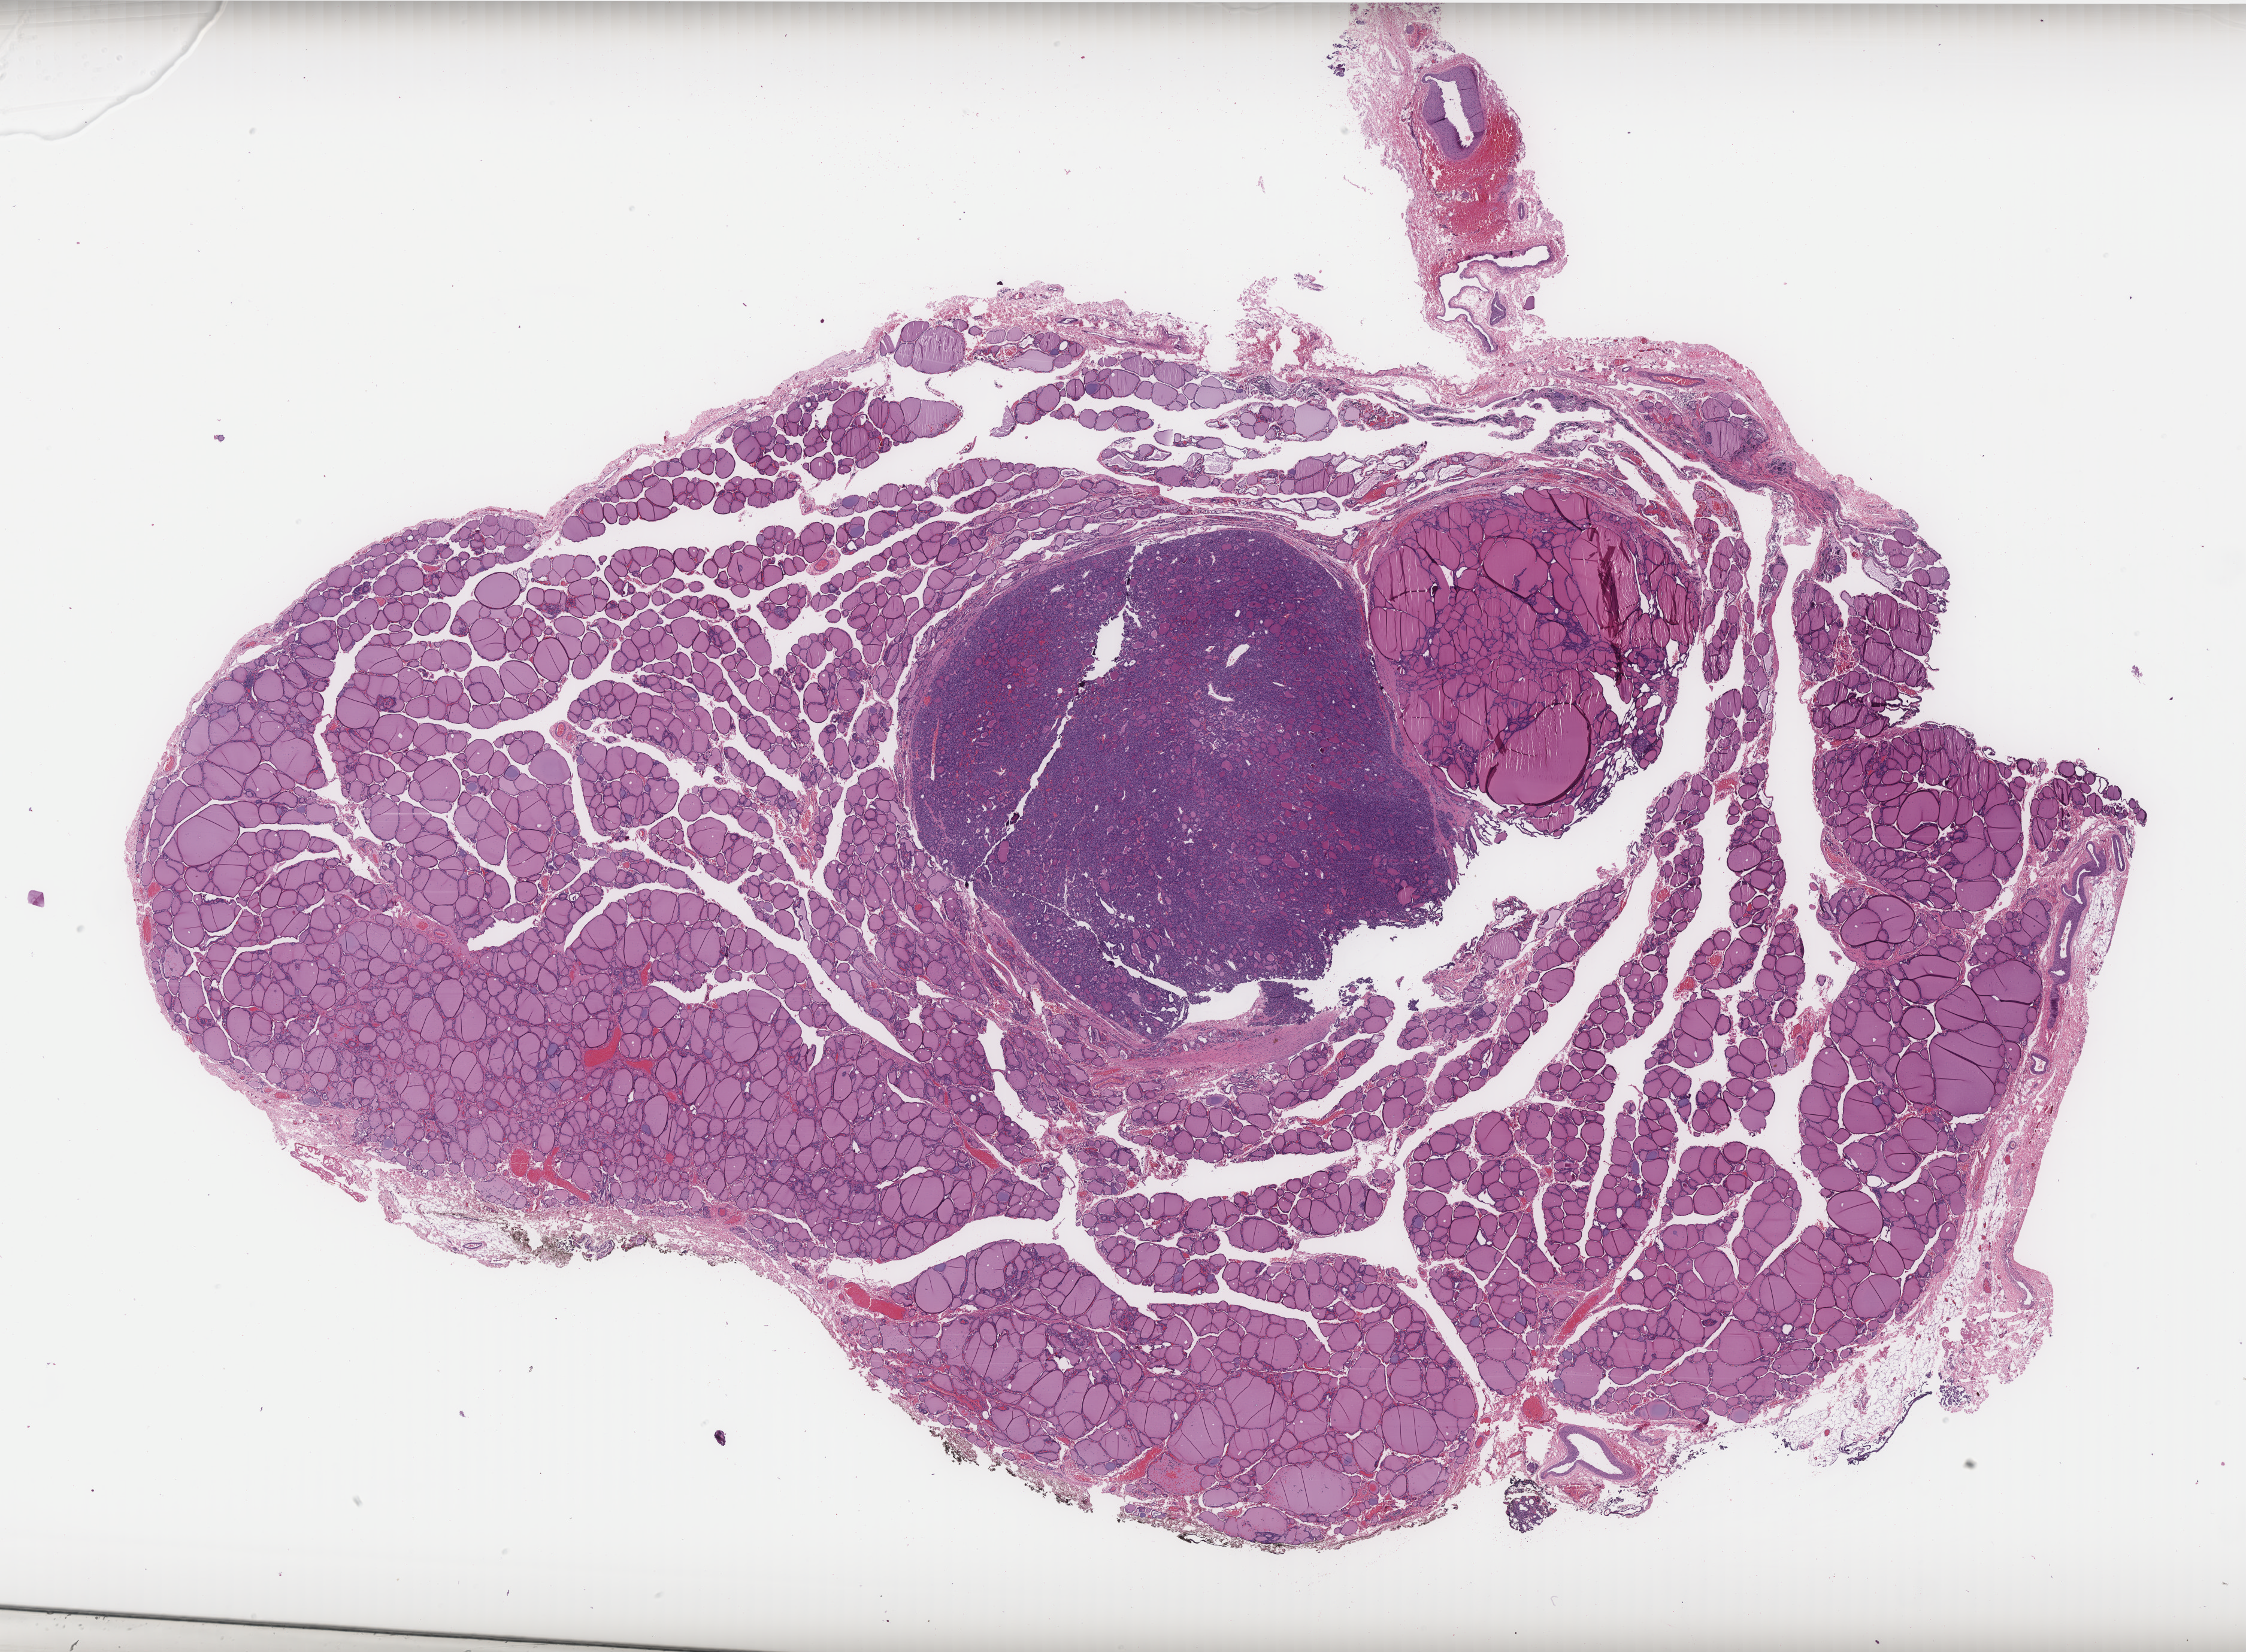
Whole-slide histology image, H&E, whole scanned area (about 30.1 x 22.1 mm) shown as a low-resolution overview. FFPE section. Primary tumour sample from the thyroid. Male patient; age at initial diagnosis 29 years.
• diagnosis: Papillary adenocarcinoma, NOS (thyroid gland)
• lymph nodes positive (case pathology): 0 of 5 examined
• AJCC pathologic stage: I